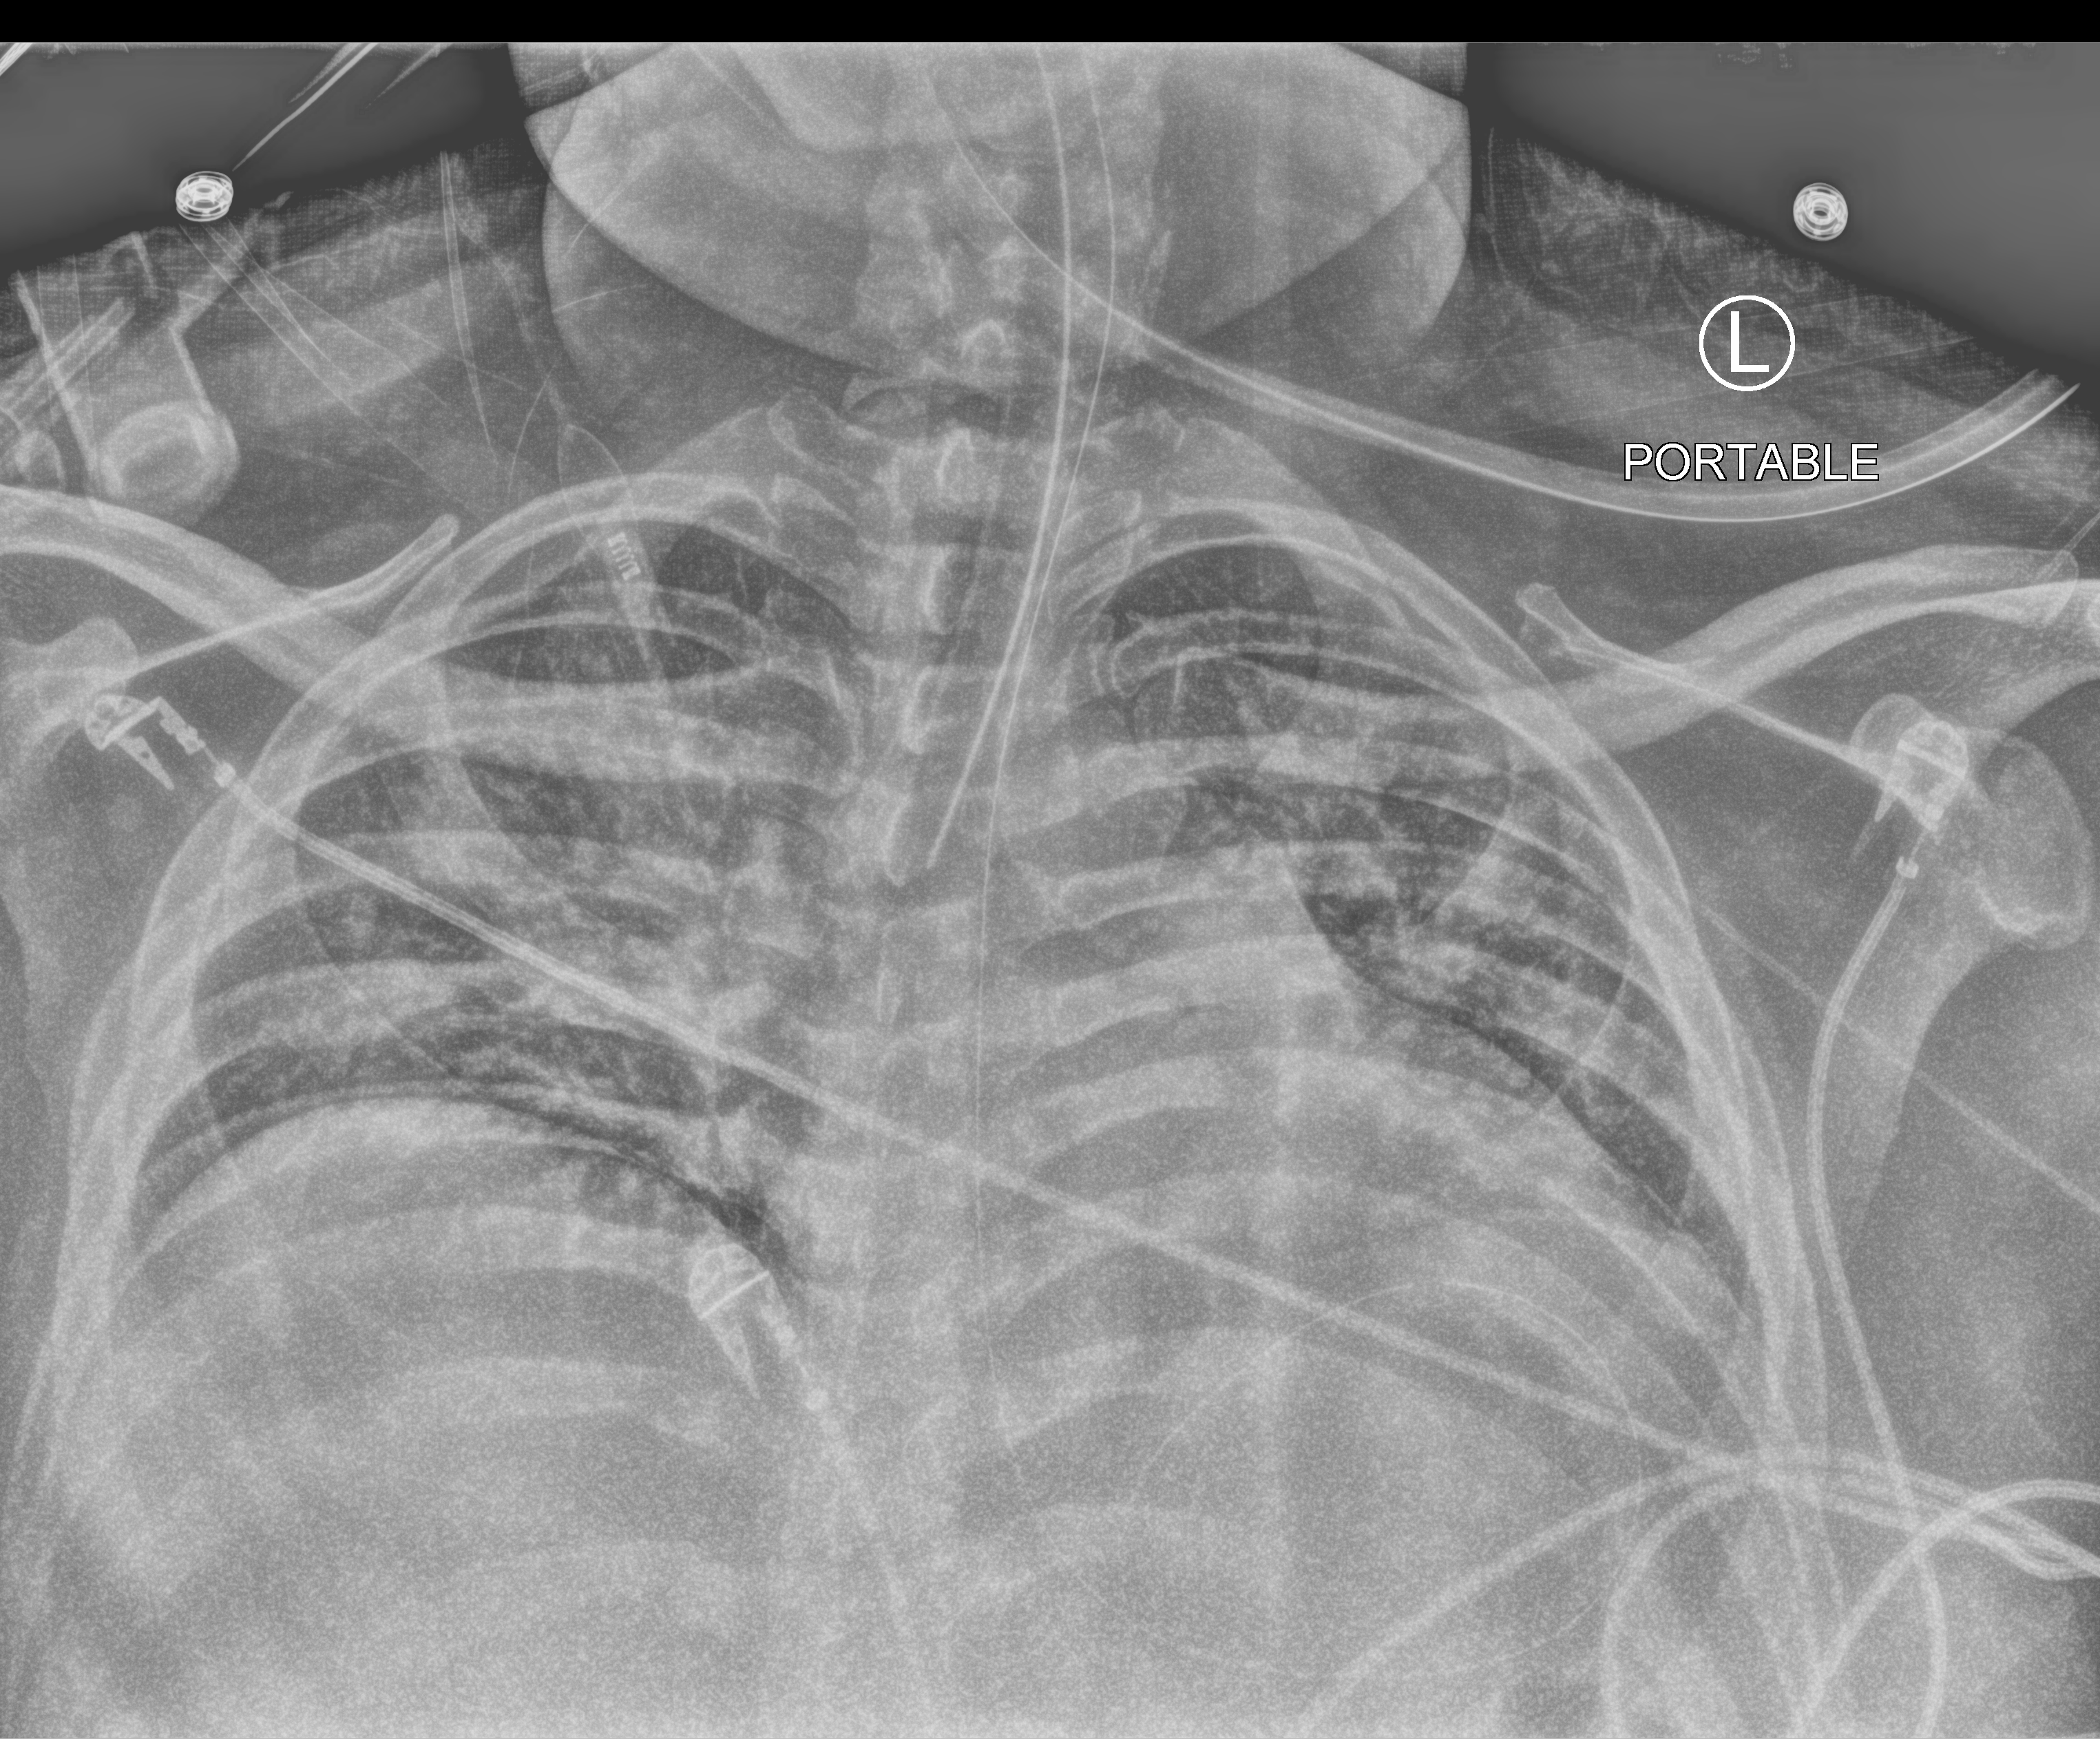
Bedside chest radiograph (computed radiography). Male patient hospitalised with COVID-19, age 18–59 years.
From the hospital-stay record, not from the radiograph (when in the stay this image was taken is not recorded):
- COPD (admission record): yes
- mechanically ventilated during this hospital stay: yes
- admitted to intensive care during this hospital stay: yes